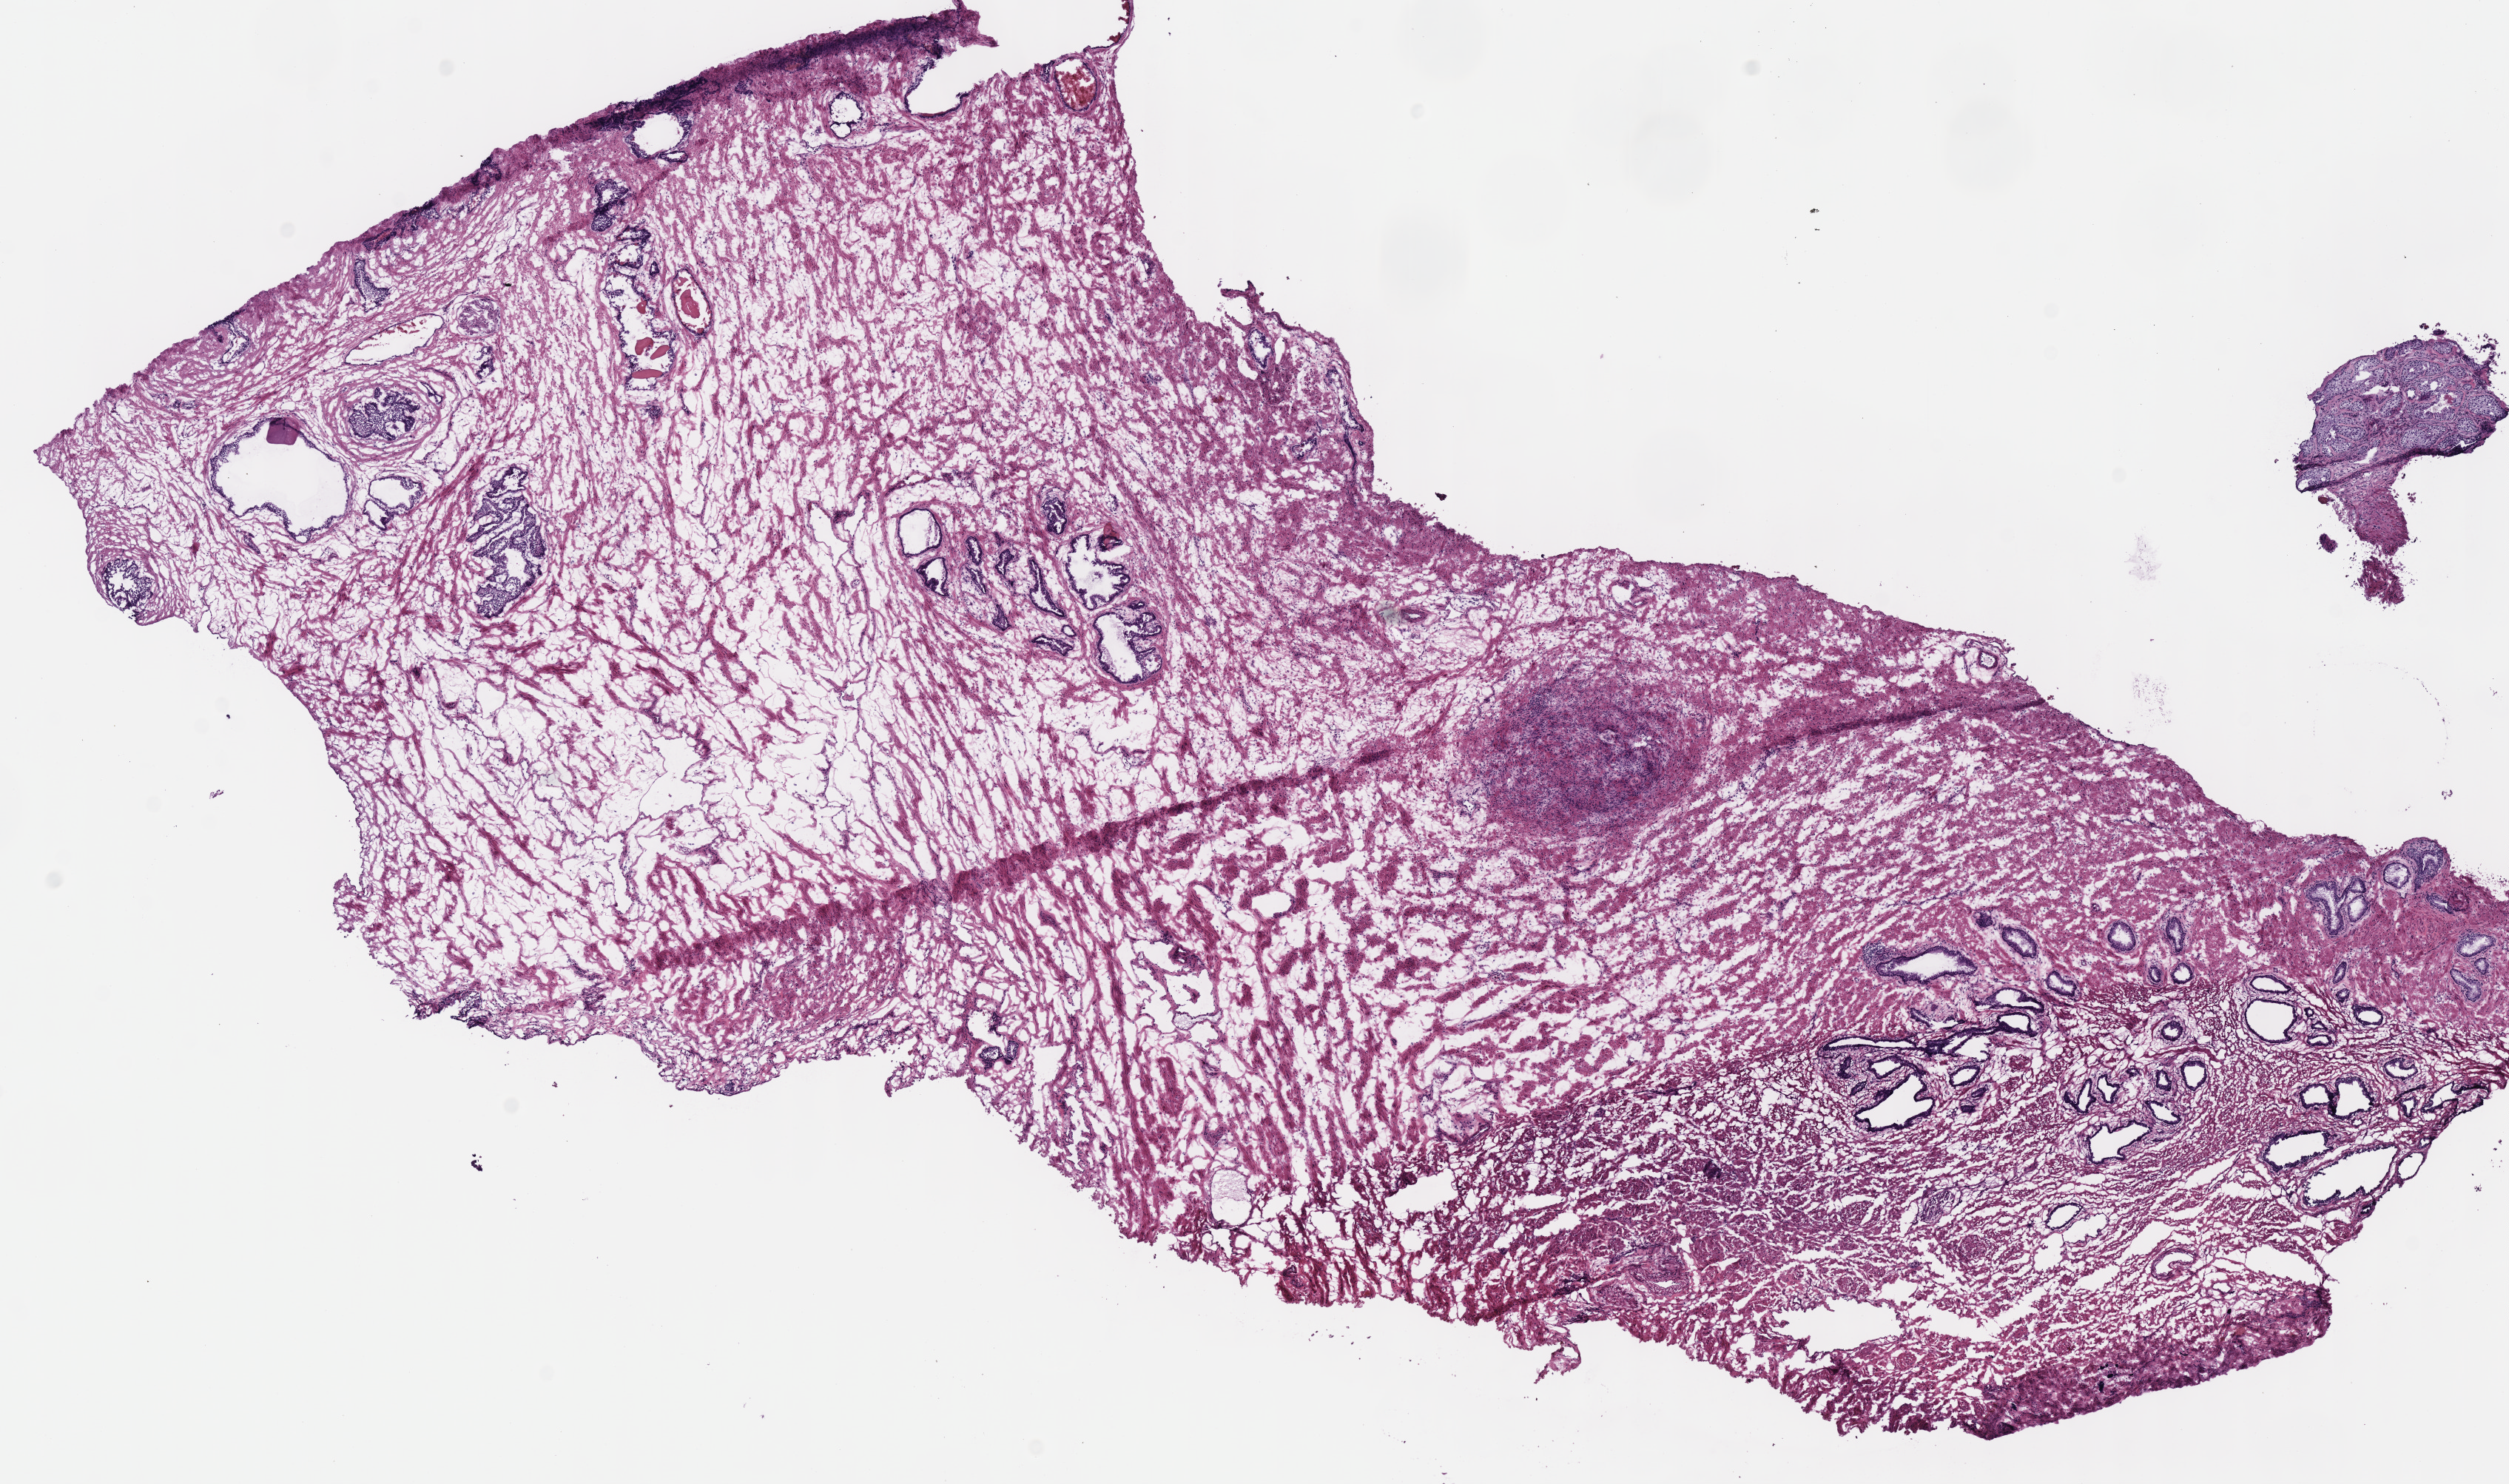
Whole-slide histology image, H&E-stained — low-resolution overview of the scanned area, about 13.4 x 7.9 mm (slide scanned at 40x); frozen section from the top of the tissue portion; prostate, solid tissue normal (non-tumour tissue) sample. Male, age 68 years at initial diagnosis.
This section: solid tissue normal sample (biorepository sample class). Patient diagnosis: Acinar cell carcinoma (prostate gland).